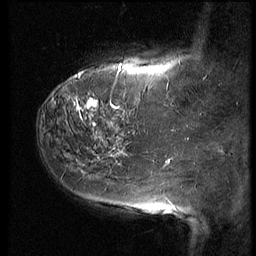
Breast MRI (dynamic contrast-enhanced), one sagittal slice. Slice 15 of 64 in the series (ordered by position). 3 images stored at this slice position (order not interpretable as contrast timing). 1.5 T. TE 4.2 ms, TR 9 ms. 256 × 256 image matrix, field of view 180 × 180 mm. Patient: female, 59 years. From the clinical record (not read from this slice): setting: breast cancer imaged before/during neoadjuvant chemotherapy; receptor status: HER2-positive.
Outlined on this slice (semi-automatic segmentation, software-assisted and operator-edited):
- analysis volume of interest (the breast-tissue region the enhancement analysis was run in; not a lesion): bounding box (x1, y1, x2, y2) in pixels: (54, 65, 155, 132)
- tumour enhancement mask (voxels above the 140 % enhancement threshold inside the analysis volume of interest): (64, 76, 121, 108)